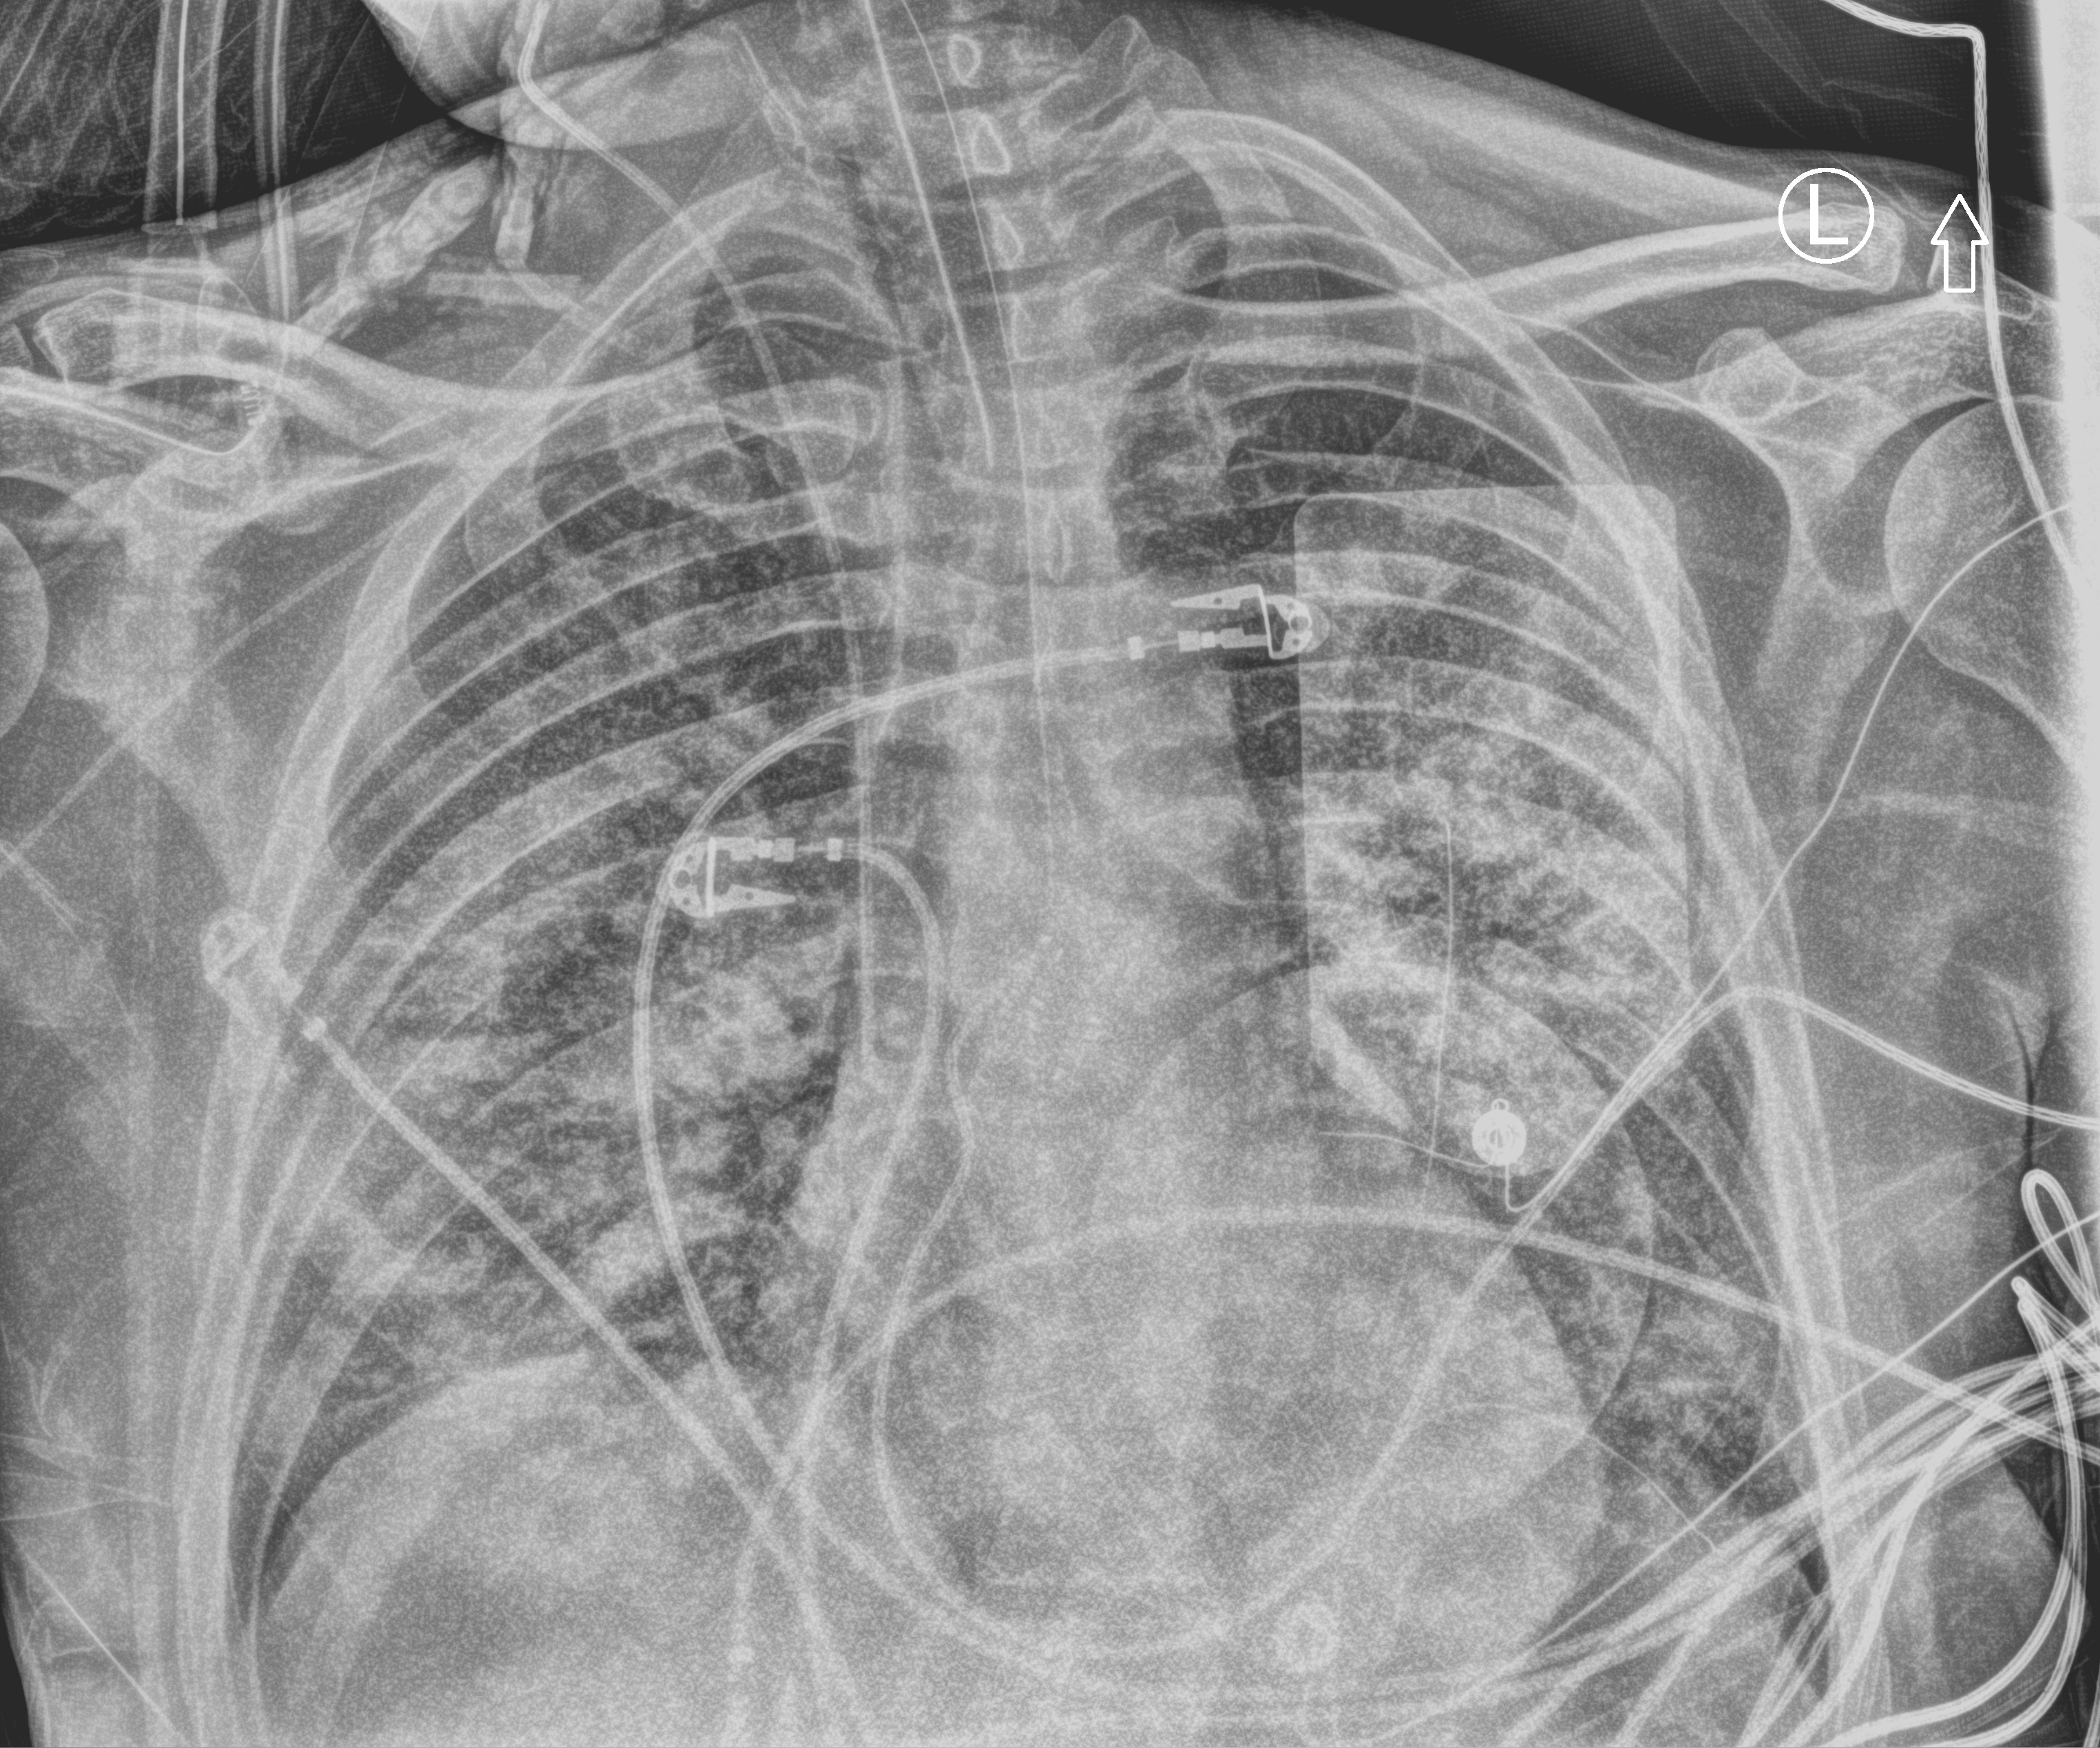
Portable chest radiograph. Patient hospitalised with COVID-19; male, aged 18–59 years.
From the hospital-stay record, not from the radiograph (when in the stay this image was taken is not recorded): mechanically ventilated during this hospital stay: yes; hypertension (admission record): no; length of hospital stay: 75 days.